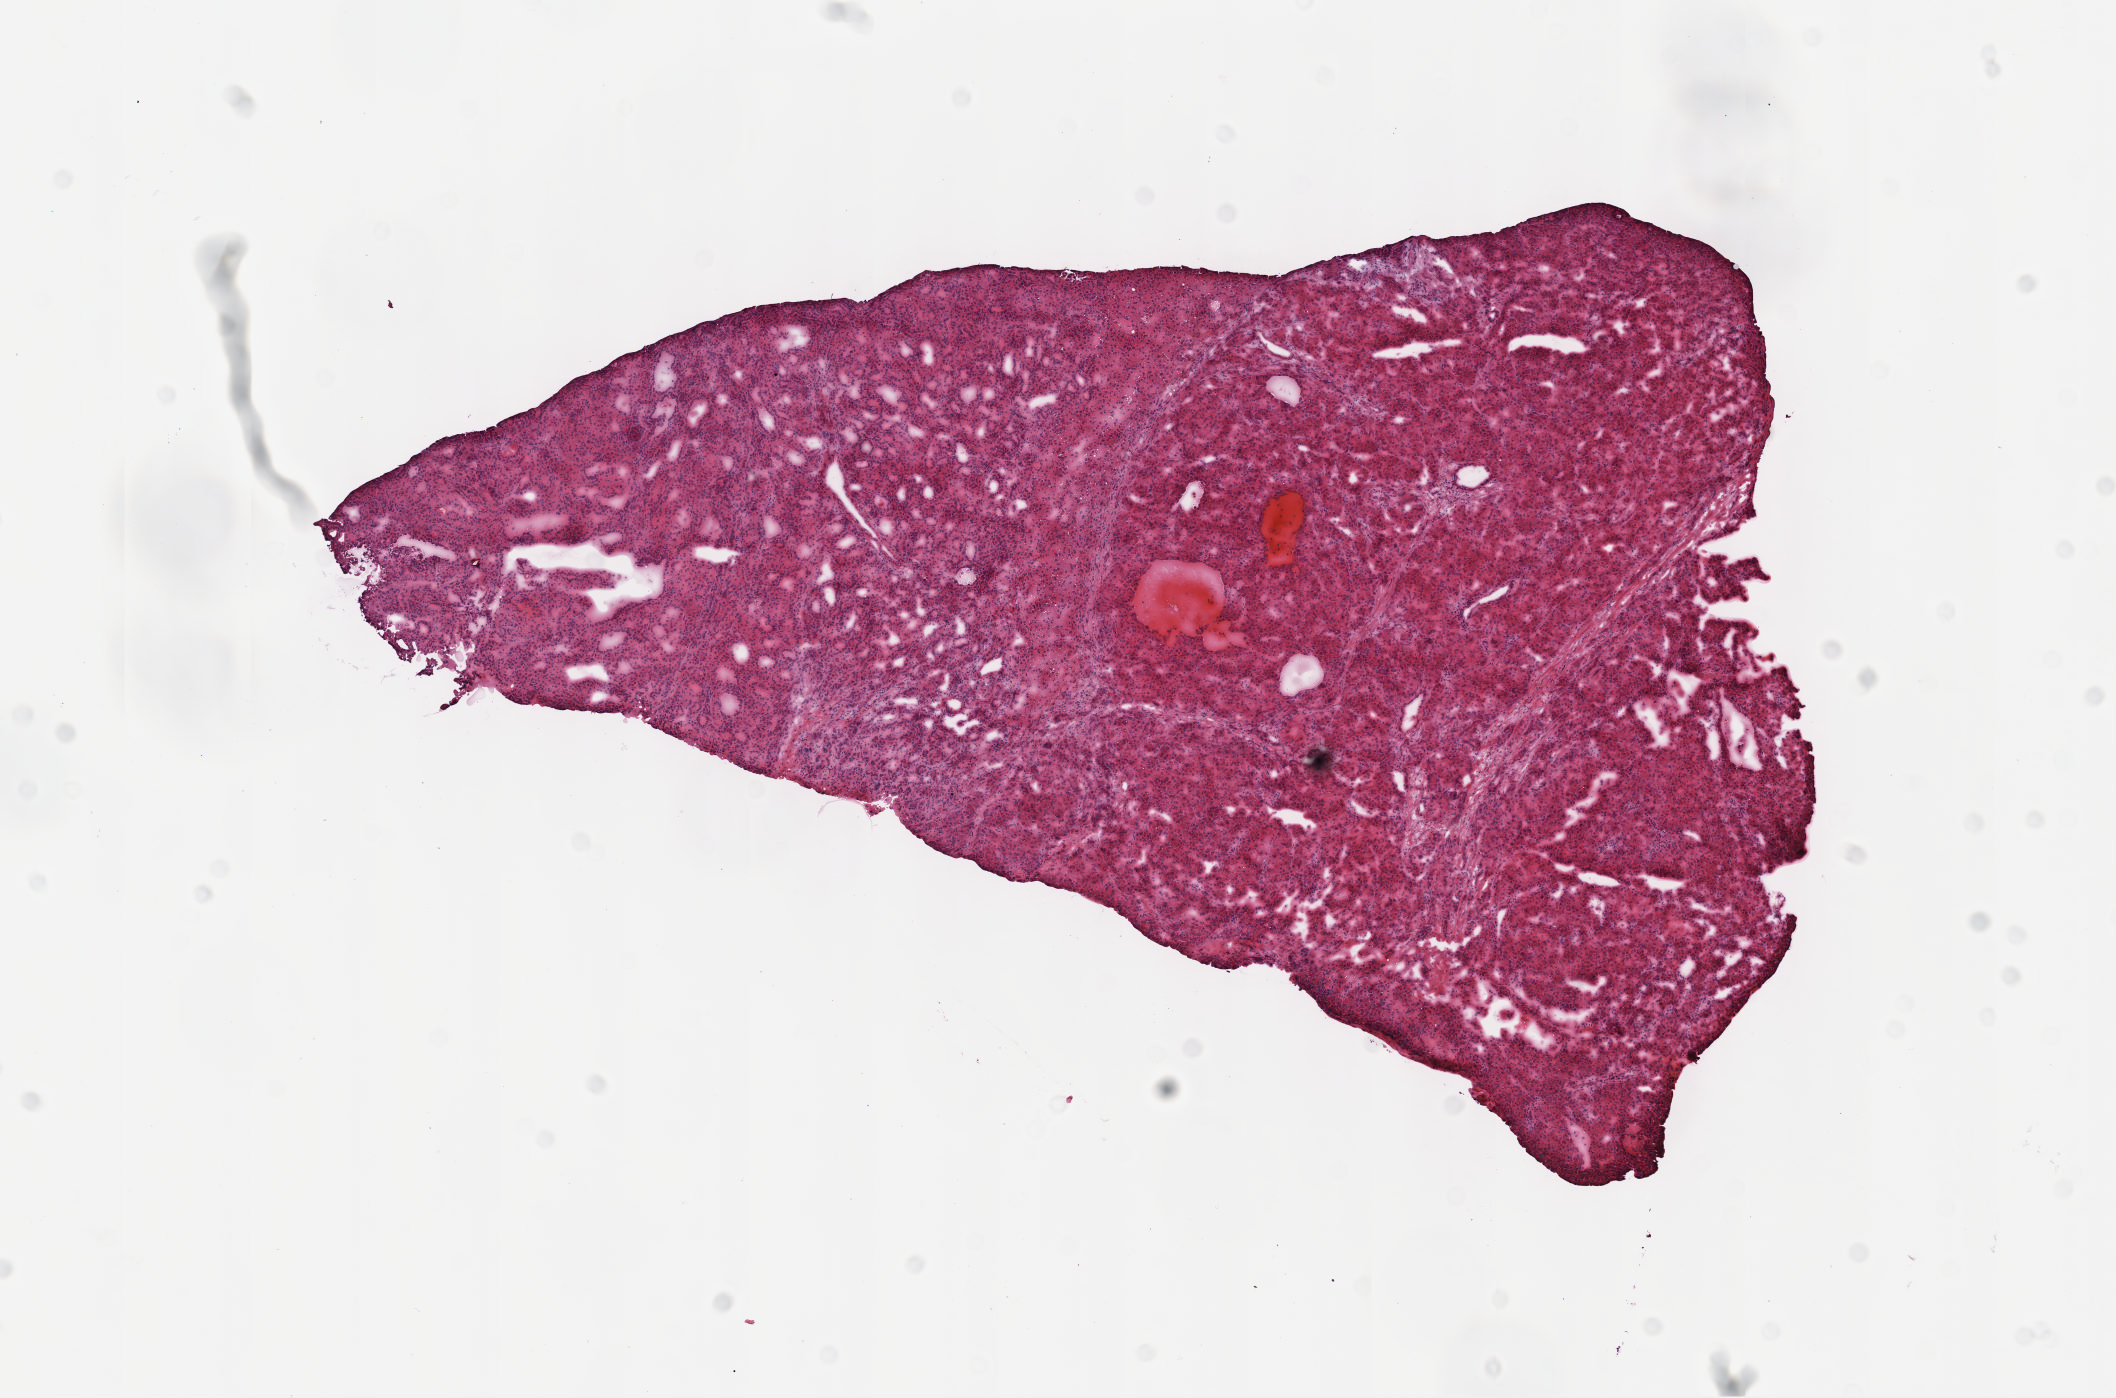
Whole-slide histology image, H&E, shown as a low-resolution overview of the whole scanned area (about 8.6 x 5.7 mm, from a 40x scan); frozen section from the top of the tissue portion; liver, primary tumour sample. Patient: male, age at initial diagnosis 58 years.
Diagnosis: Hepatocellular carcinoma, NOS.